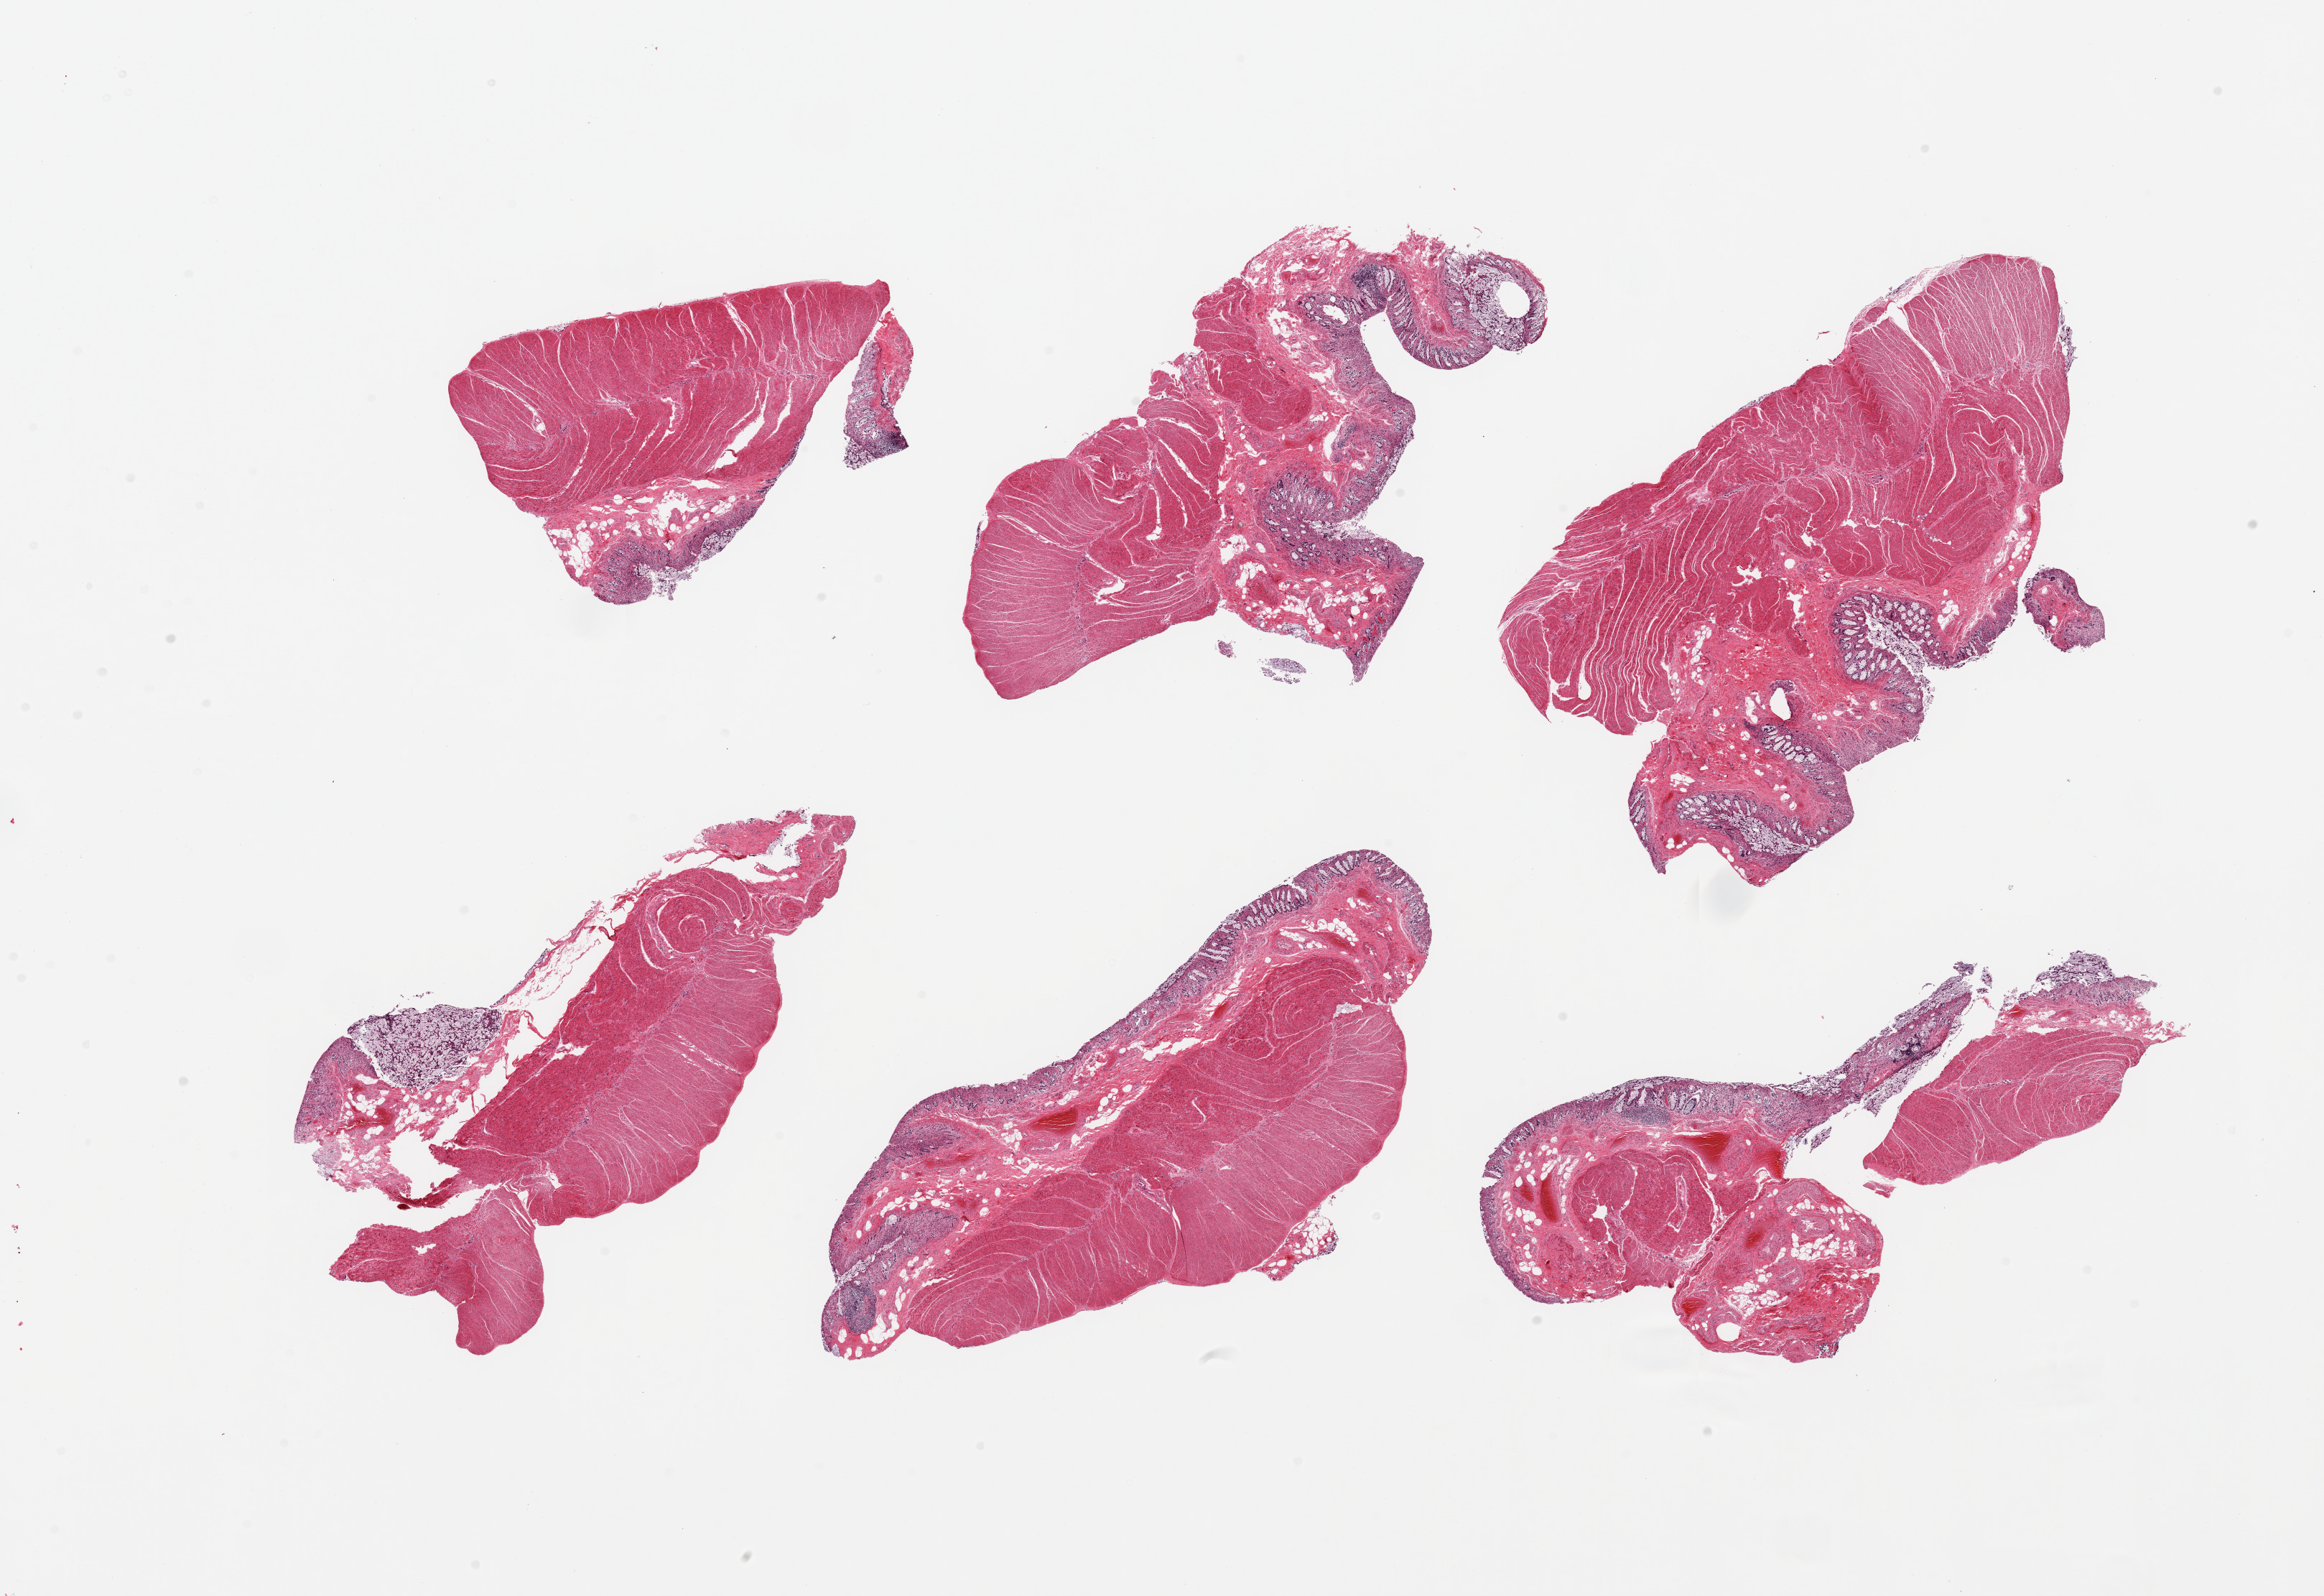
Digitized haematoxylin and eosin-stained section, brightfield, whole scanned area (about 25.6 x 17.6 mm, acquisition: 20x scan) shown as a low-resolution overview. Donor: male.
• specimen: PAXgene-fixed paraffin-embedded (PFPE) section; section of sigmoid colon (target tissue); tissue donor sample